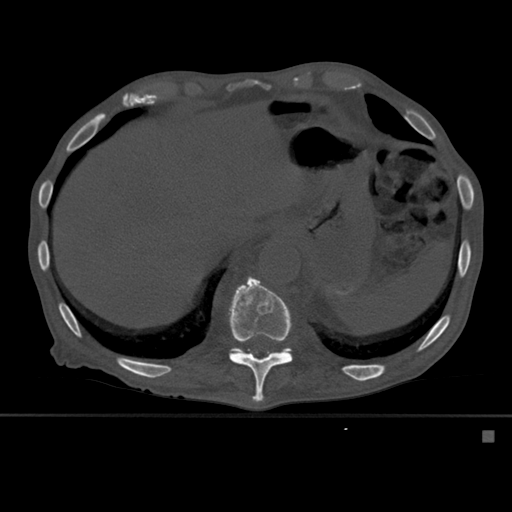
CT including the spine, one axial slice. Position 293 of 527 along the scan axis. Bone window (W 1800 / L 400 HU). 512 × 512 image matrix, field of view 373 × 373 mm. Patient: male, 78 years. Case-level facts recorded for this patient, not image findings: primary cancer: prostate.
Structures marked on this image (semi-automatically segmented with operator editing):
- T11 vertebra: bounding box <229,276,293,403> (left, top, right, bottom; pixels)
- T12 vertebra: <229,348,291,356>